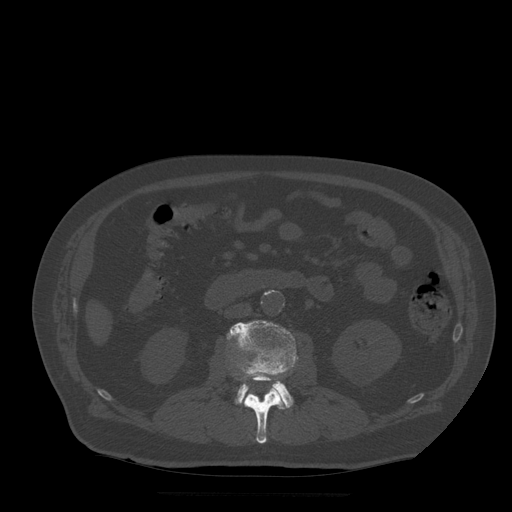
CT including the spine, one axial slice. Slice 157 of 522 in the series (ordered by position). Bone window (W 1800 / L 400 HU). 1.25 mm slice thickness. 512 × 512 image matrix, field of view 420 × 420 mm. Patient age 72 years. Case-level facts recorded for this patient, not image findings: primary cancer: prostate.
Structures marked on this image (semi-automatically segmented with operator editing):
- L2 vertebra: bounding box (x1, y1, x2, y2) in pixels: (240, 372, 286, 444)
- L3 vertebra: (227, 320, 298, 408)